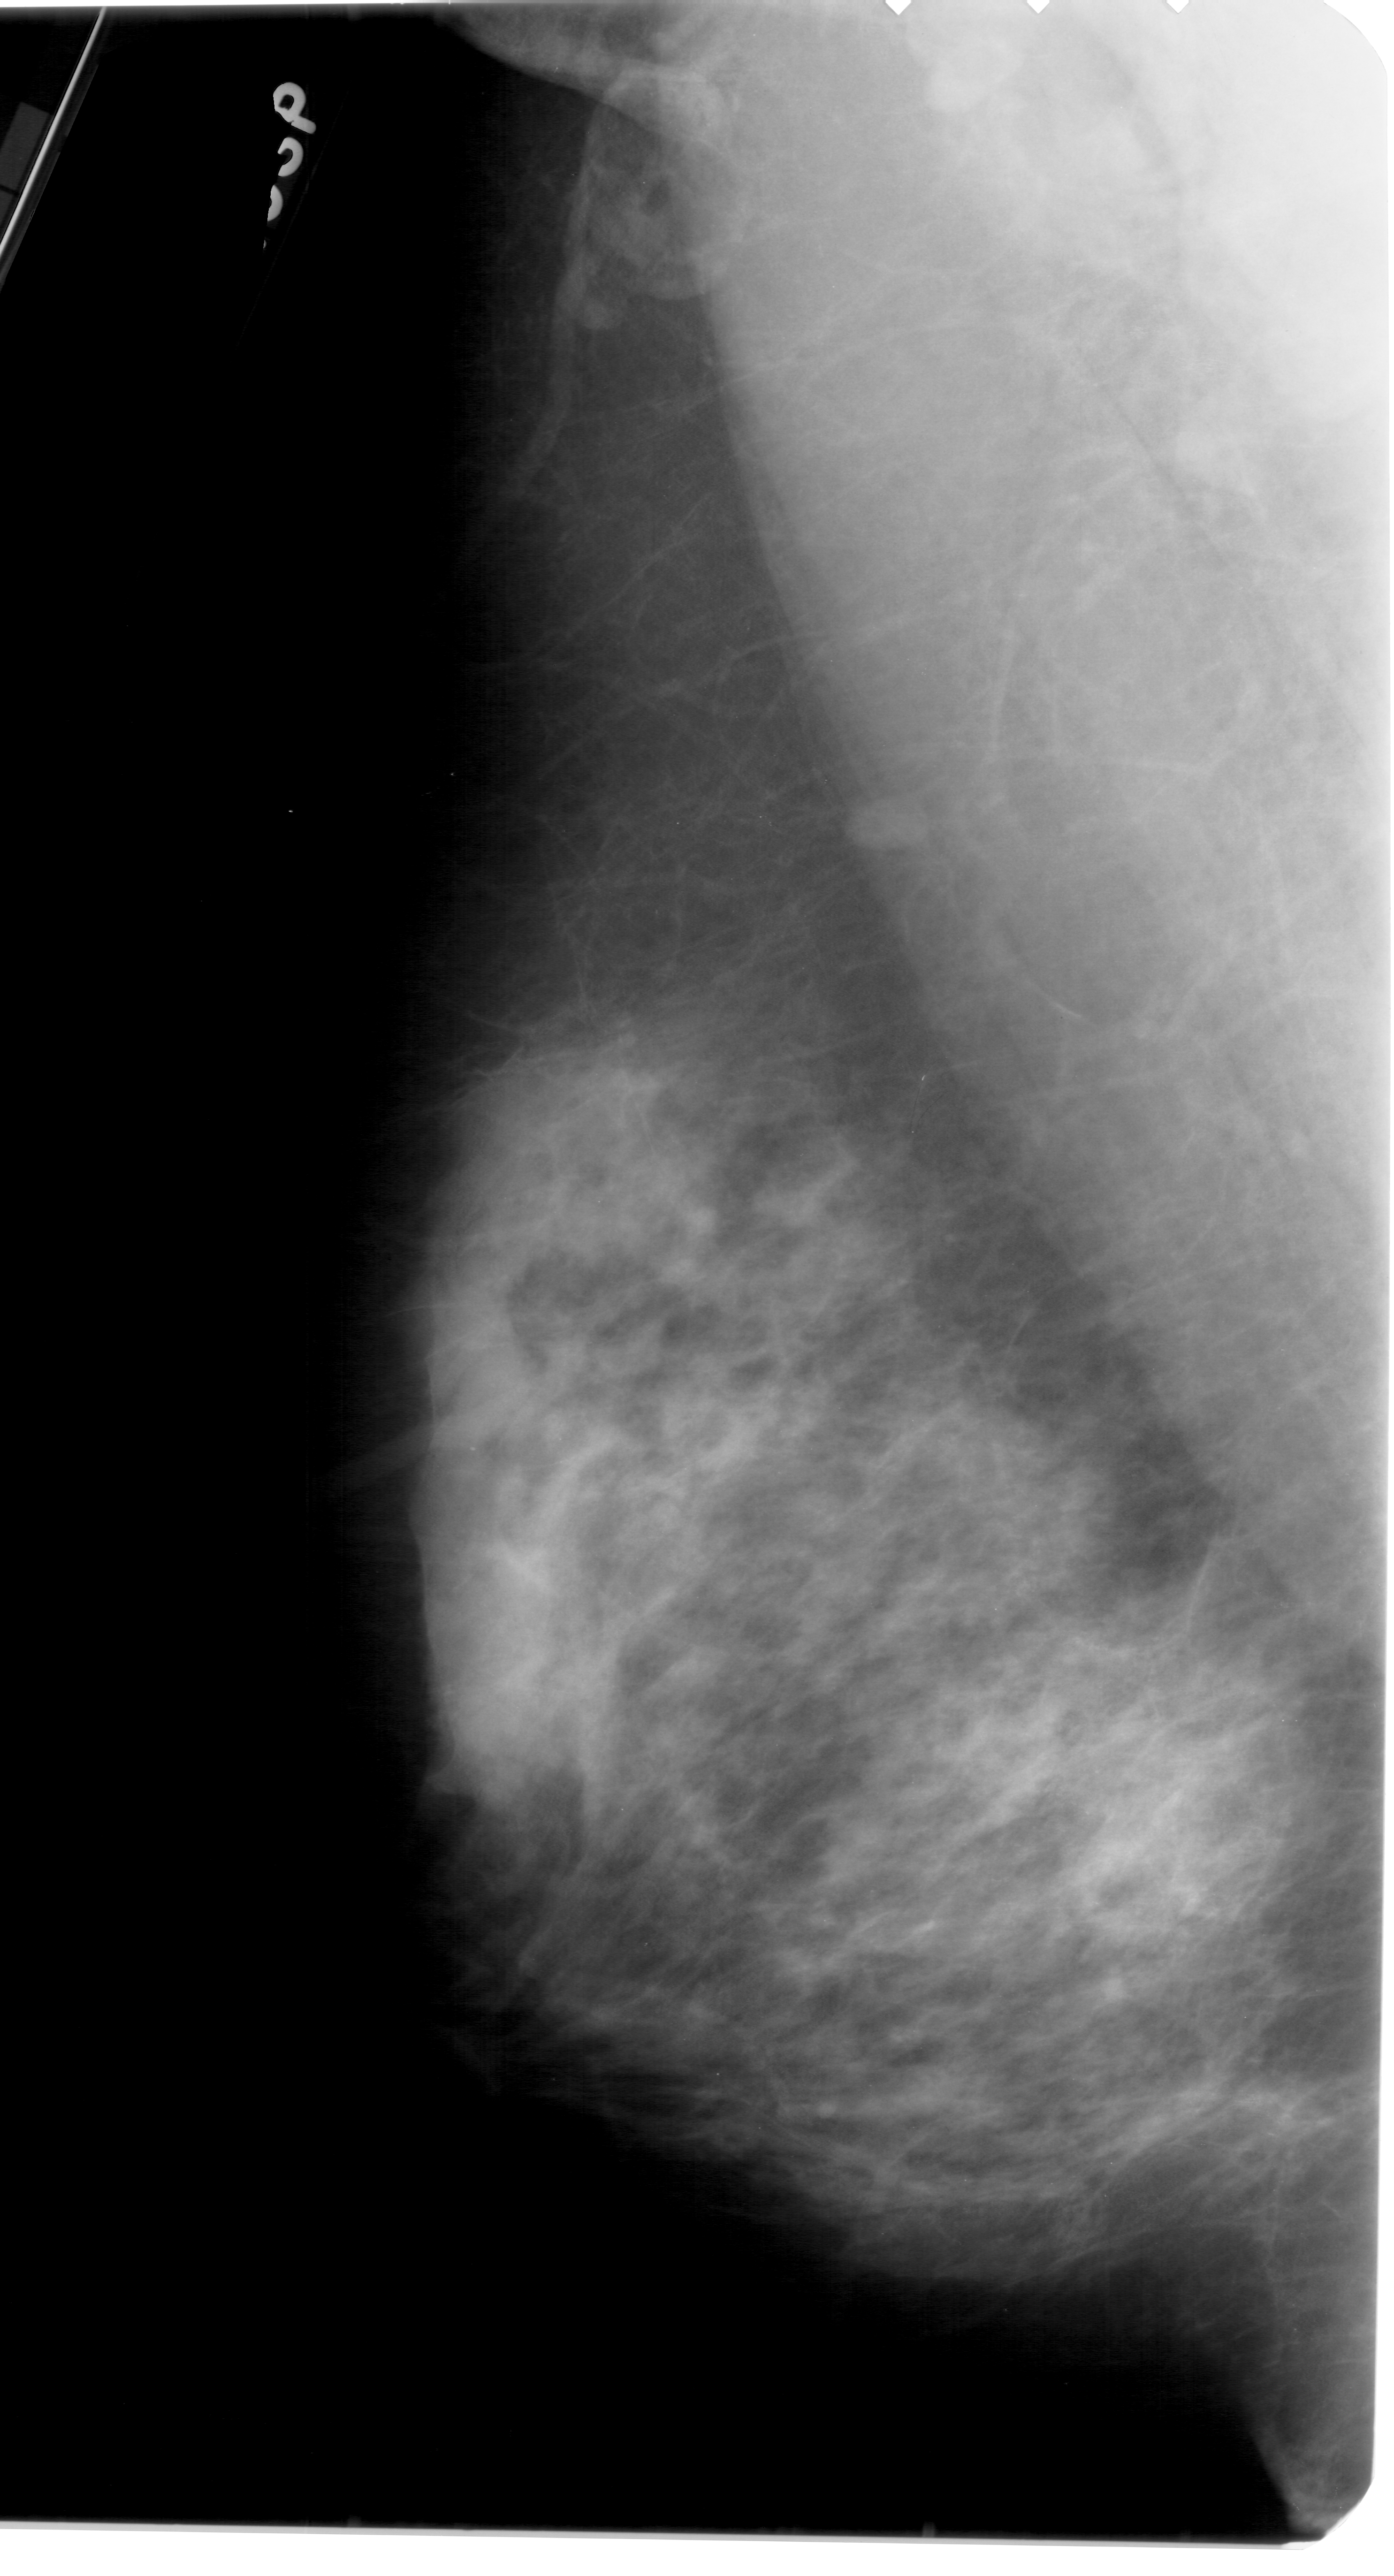
Scanned film-screen mammogram. Left breast. Mediolateral oblique (MLO) view. BI-RADS breast density category 3 (scale 1–4). 1394 × 2576 image matrix.
Expert-marked regions of interest on this image (one box per marked abnormality):
- calcifications, morphology pleomorphic, distribution segmental; BI-RADS assessment category 4; pathology (as recorded): benign: box from (x=807, y=1619) to (x=1255, y=2018) px